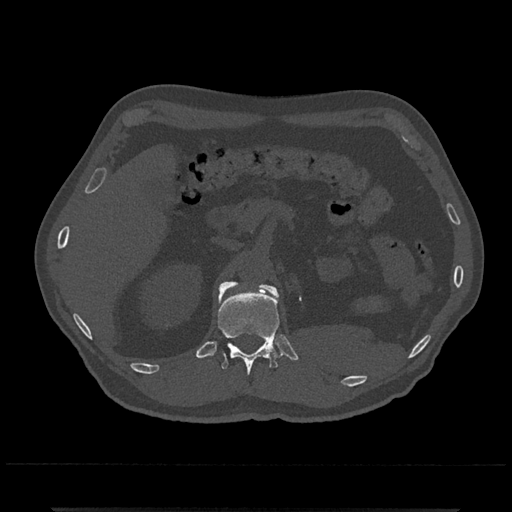
CT including the spine, one axial slice. Slice 421 of 797 in the series (ordered by position). 120 kVp. Bone window (W 1800 / L 400 HU). 0.5 mm slice thickness. 512 × 512 image matrix, field of view 393 × 393 mm. Patient: male, 67 years. Case-level facts recorded for this patient, not image findings: primary cancer: prostate.
Annotated regions visible in this slice (semi-automatic segmentation, software-assisted and operator-edited):
- L1 vertebra: box from (x=219, y=282) to (x=277, y=295) px
- T12 vertebra: (x=217, y=282)–(x=282, y=376)